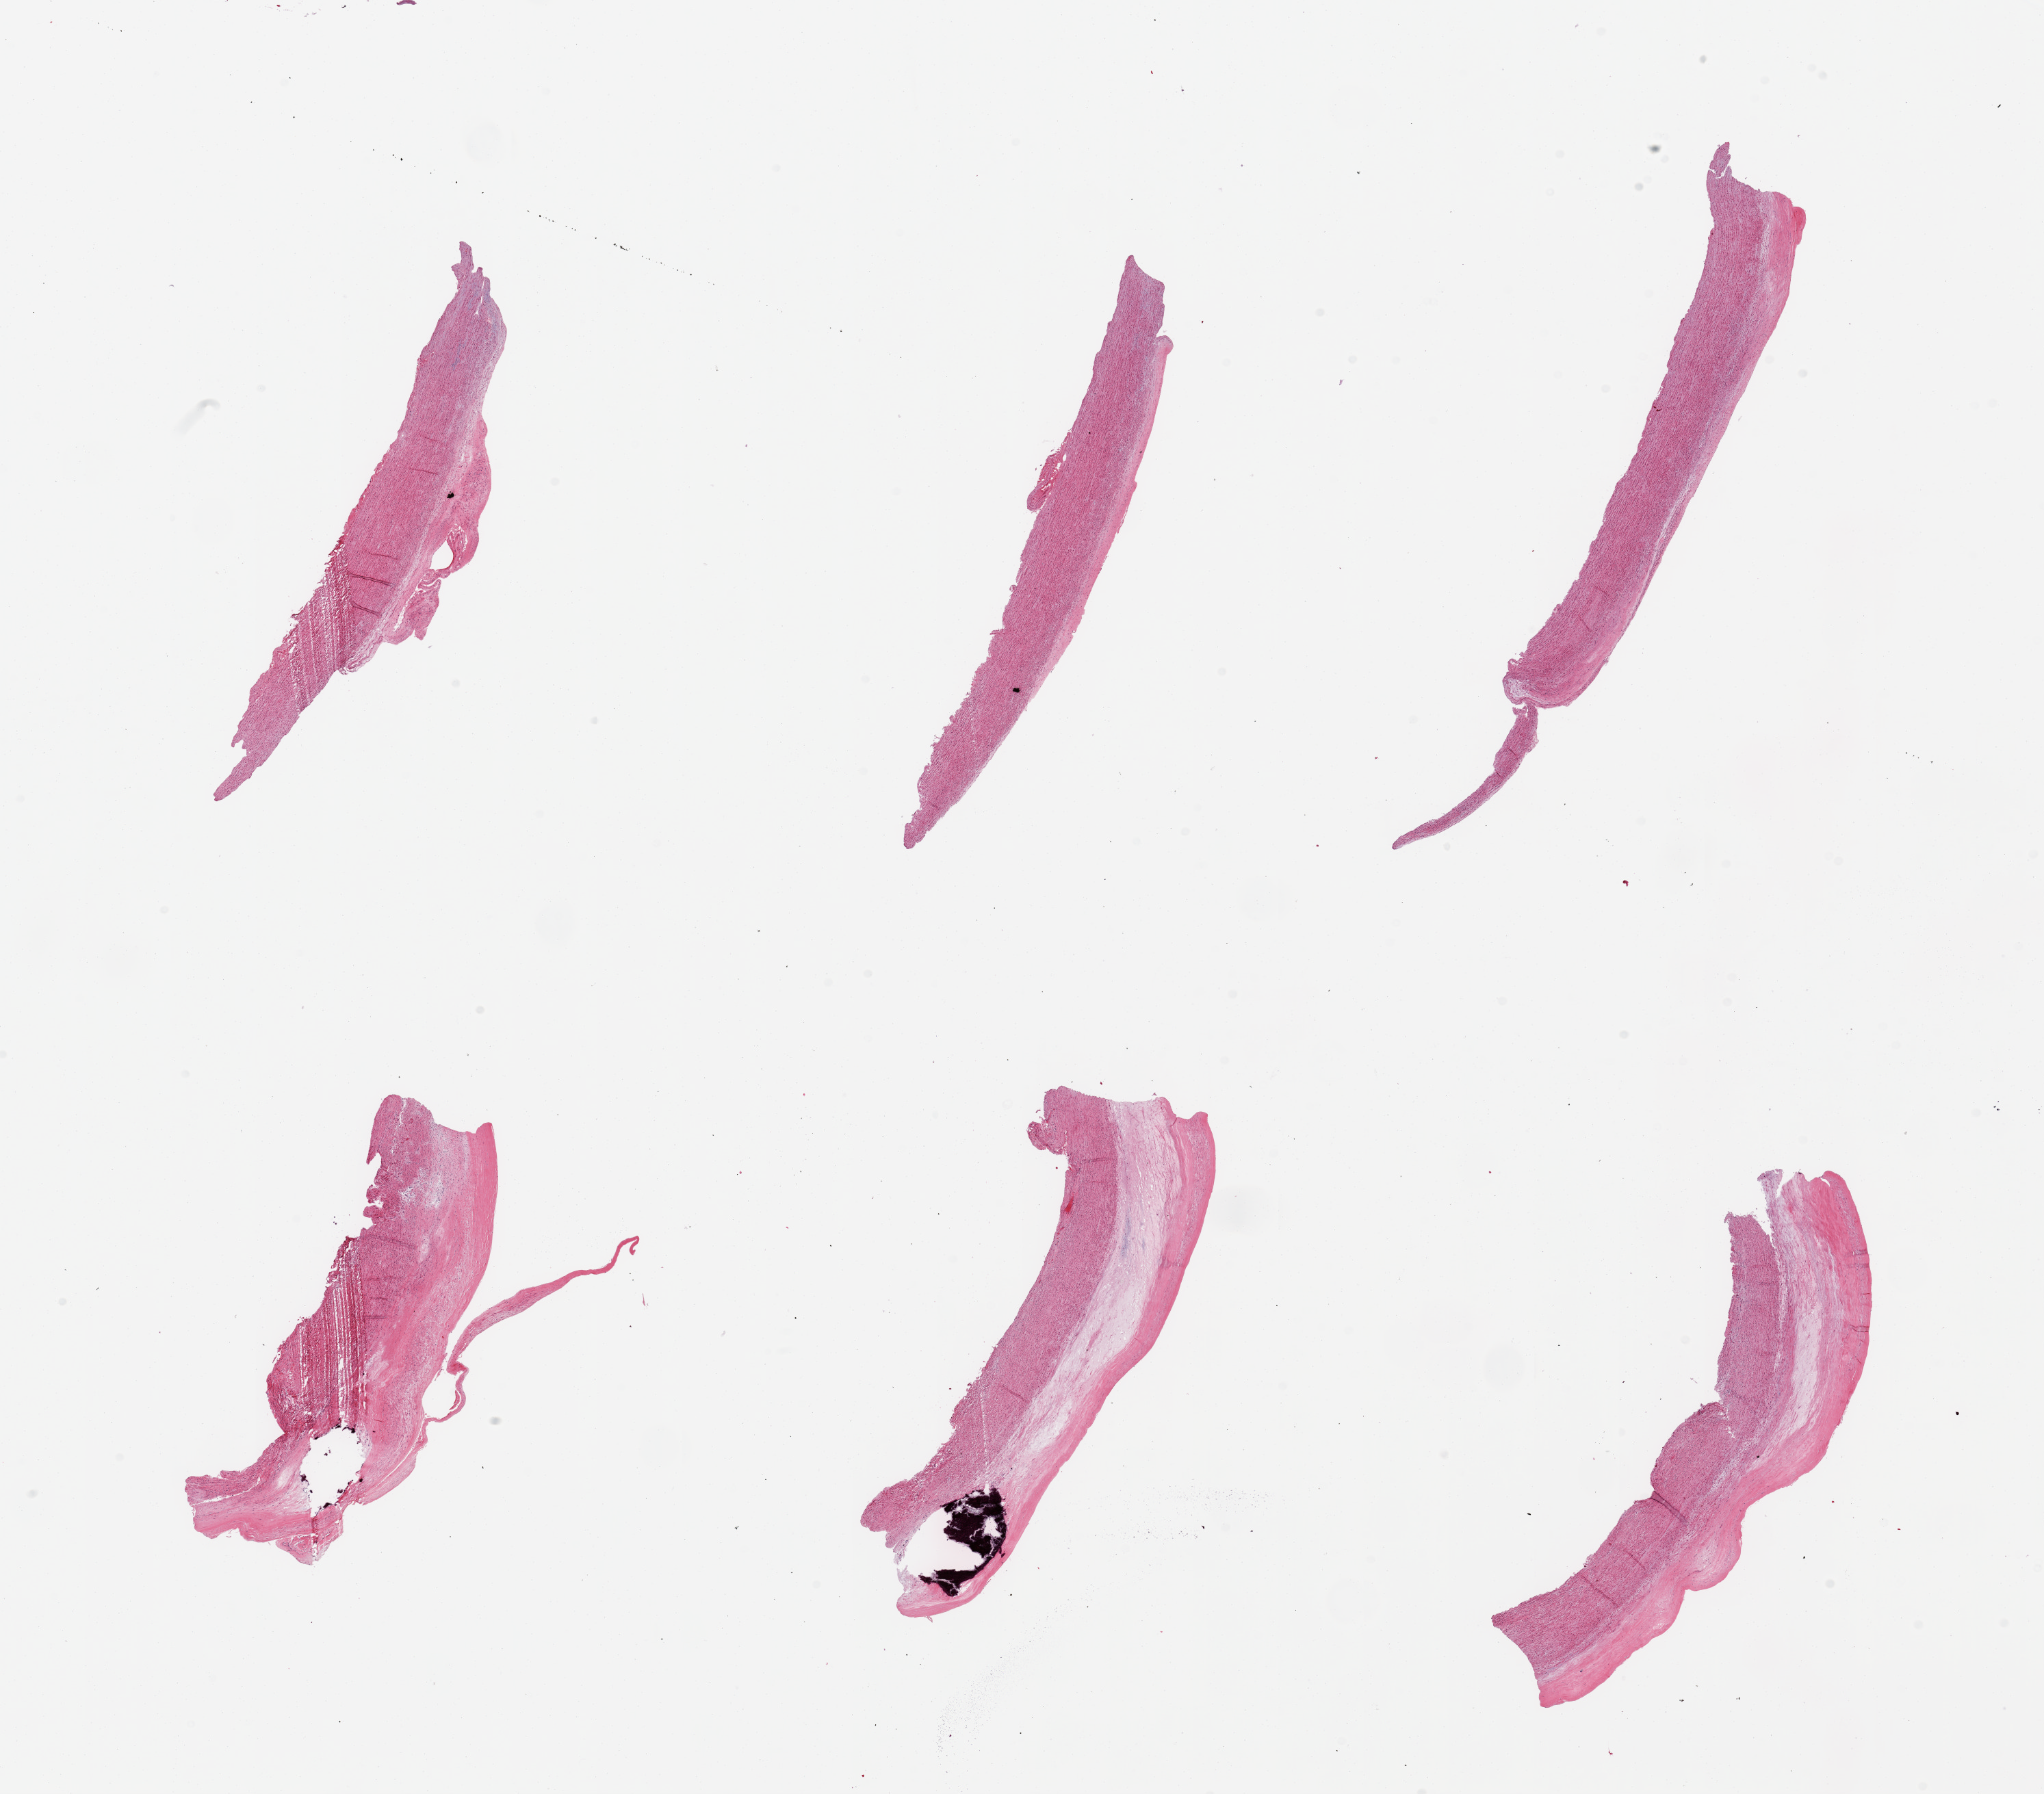
Digitized haematoxylin and eosin-stained section, brightfield, a low-resolution overview of the entire scanned area, about 23.6 x 20.7 mm. PAXgene-fixed paraffin-embedded (PFPE) section. Sampled site (target tissue): aorta. Tissue donor sample. Donor: female.
- review note (as recorded): 6 pieces, atherosis layer up to ~1mm, focally calcifying